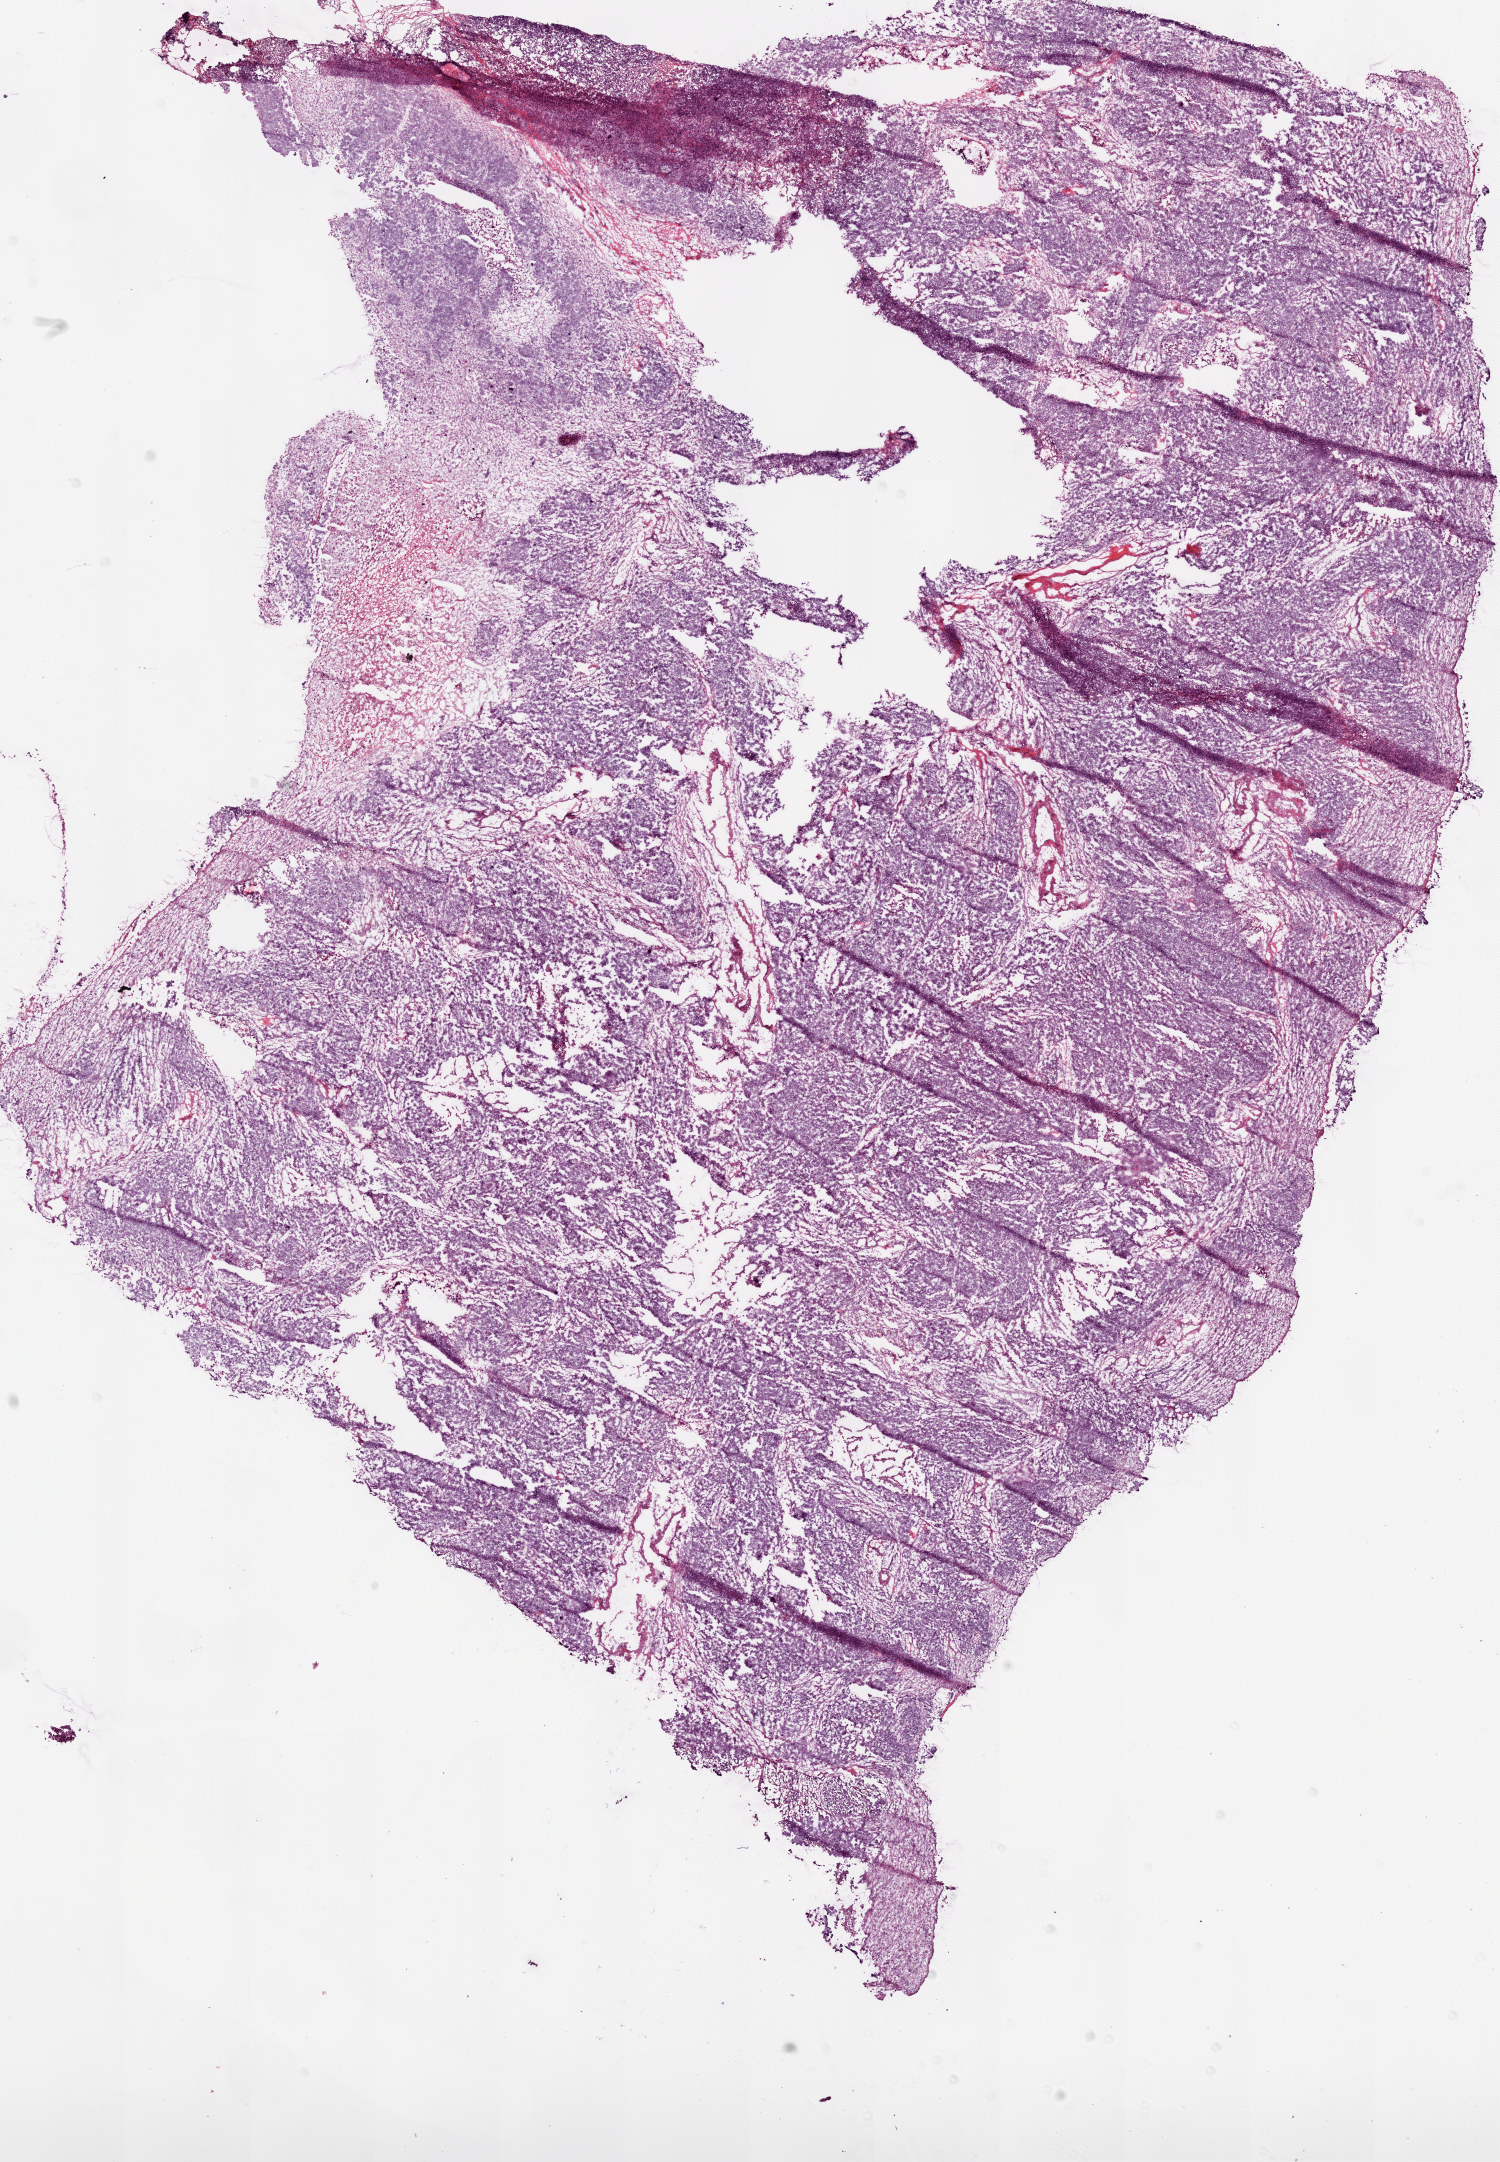
Digitized H&E-stained tissue section (whole slide) — whole scanned area (about 12.0 x 17.3 mm, slide scanned at 20x) shown as a low-resolution overview, frozen section from the bottom of the tissue portion, sample: primary tumour, ovary. Female, age 77 years at initial diagnosis. Histologic grade: G3 (poorly differentiated). Composition of this section per pathologist review: tumour cells 90%, tumour nuclei 95%, normal cells 0%, stromal cells 5%, necrosis 5%.
FIGO stage: IIIC. Laterality: bilateral. Histologic diagnosis: Serous cystadenocarcinoma, NOS.